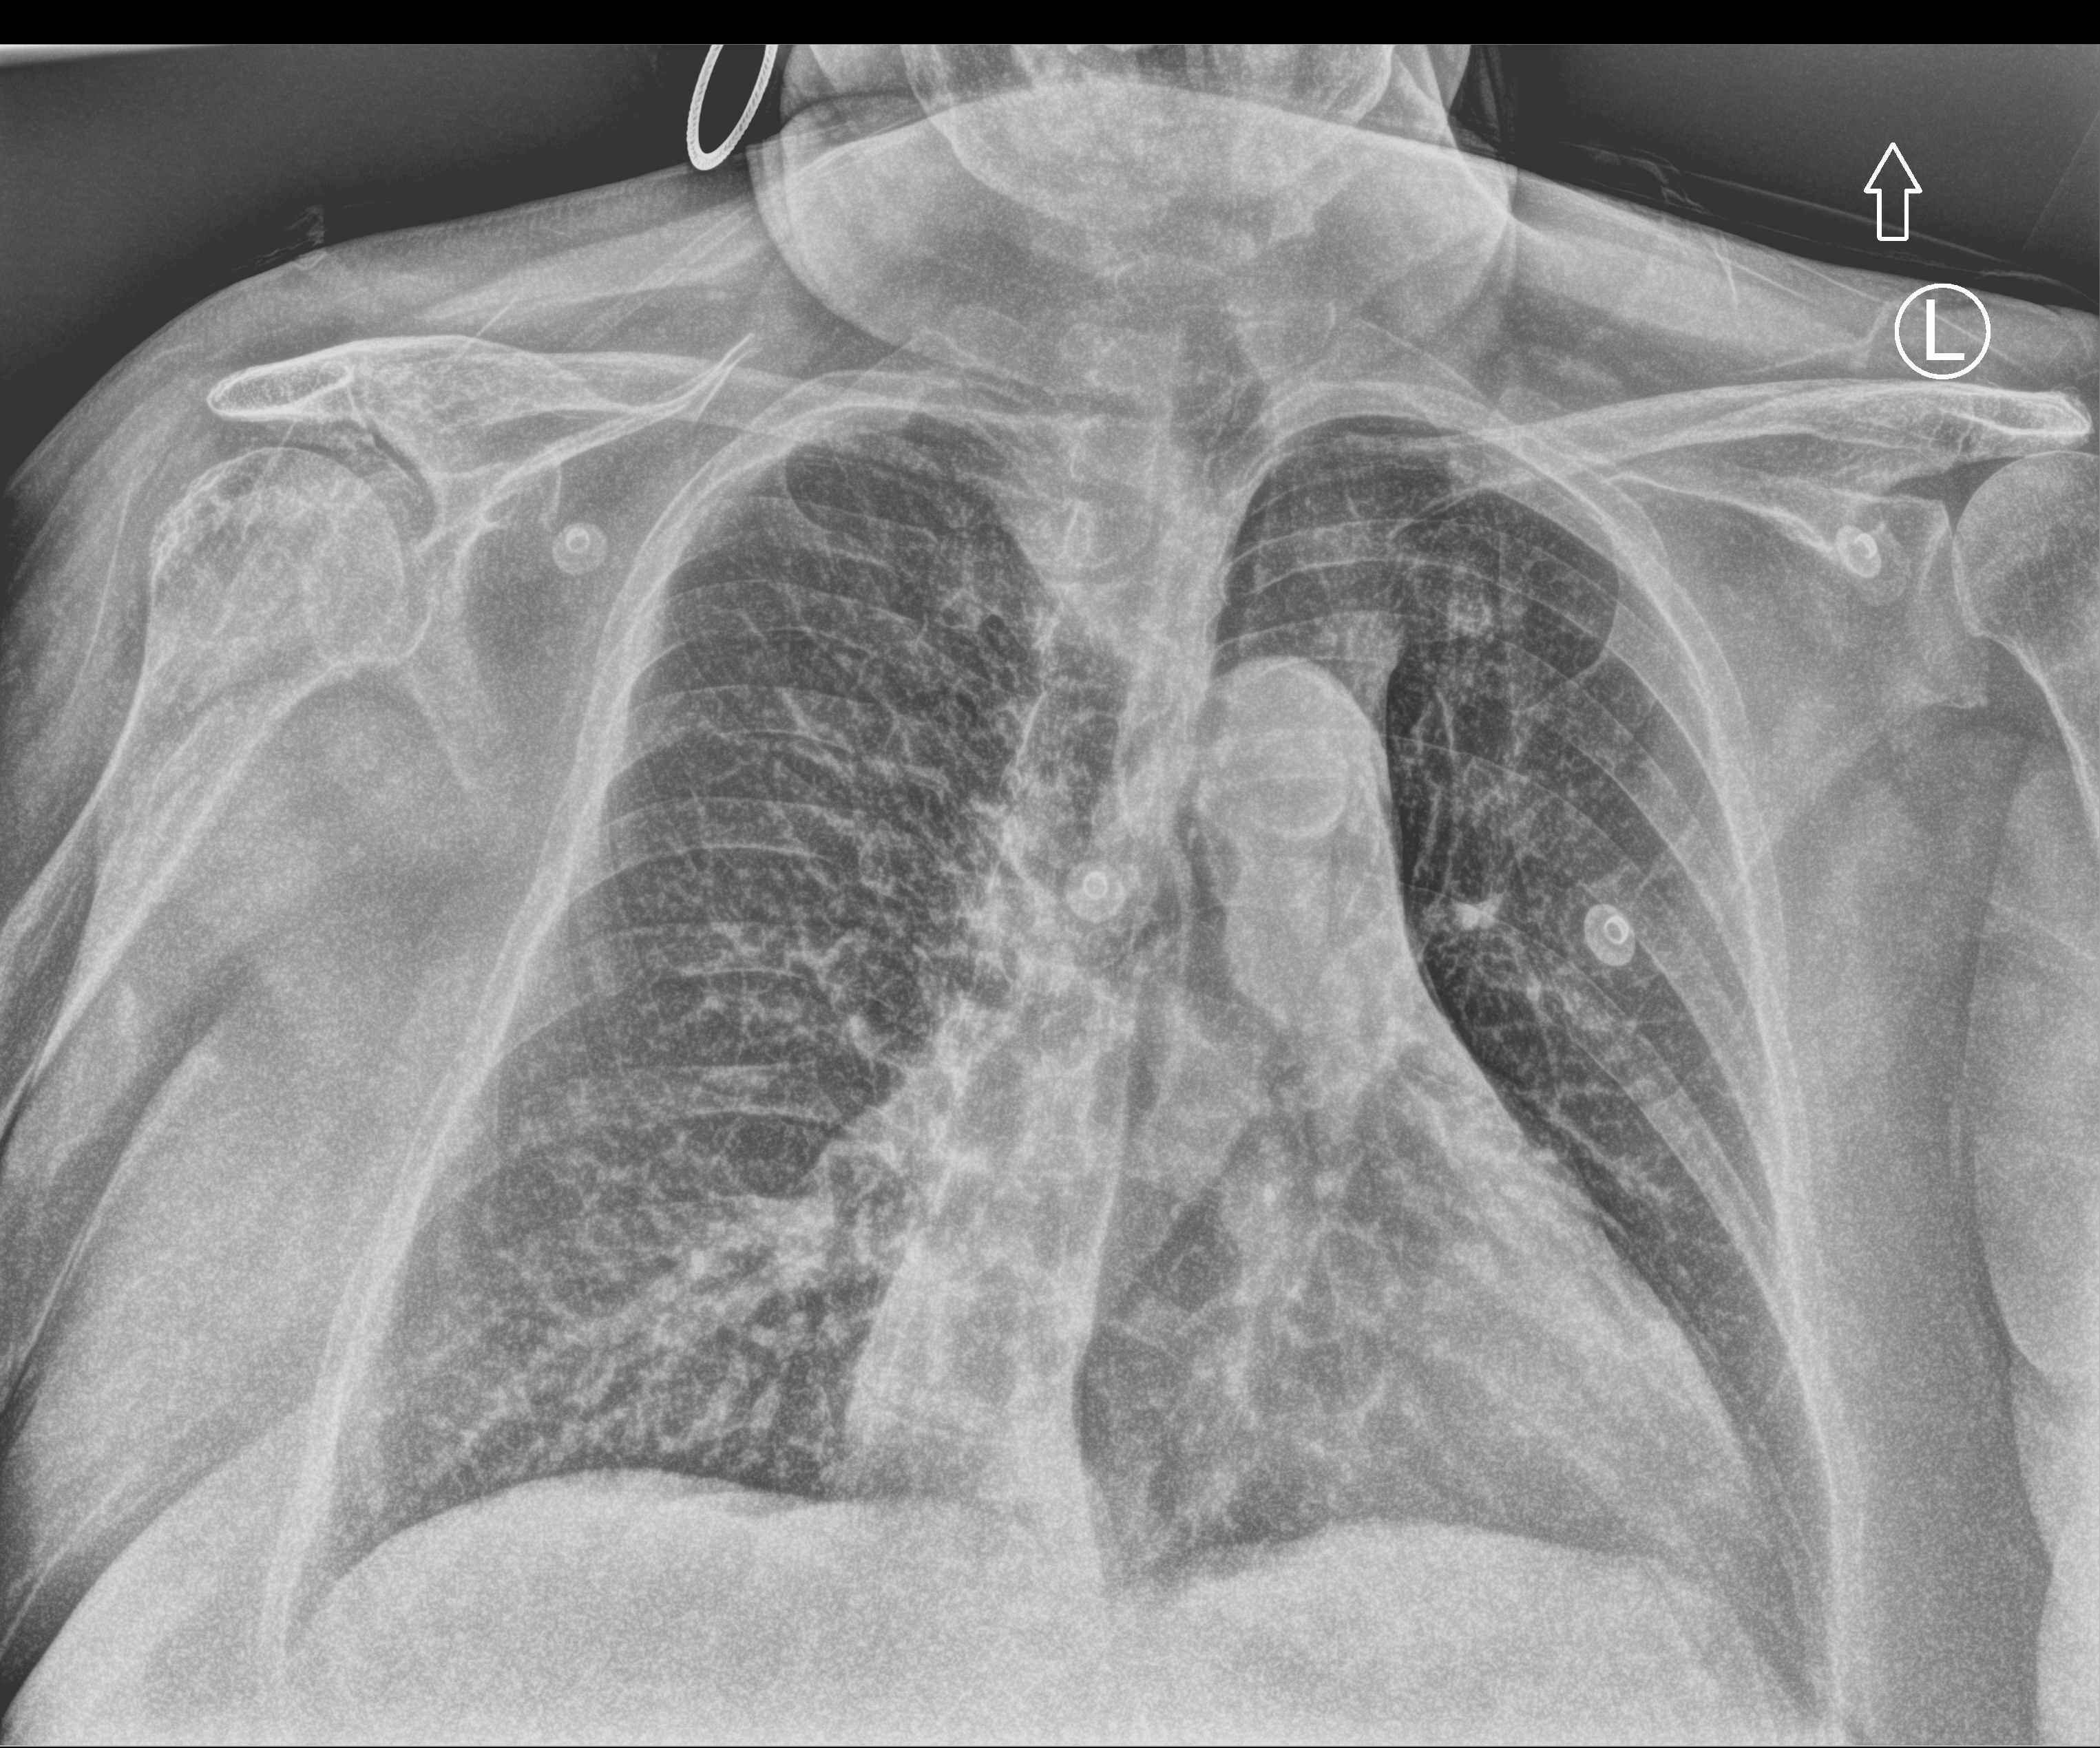
Portable chest radiograph, anteroposterior (AP) projection. Patient hospitalised with COVID-19; female, aged 60–74 years.
Hospital-stay facts (about this admission, not read from this image; timing relative to this image not recorded): admitted to intensive care during this hospital stay: yes; mechanically ventilated during this hospital stay: no.